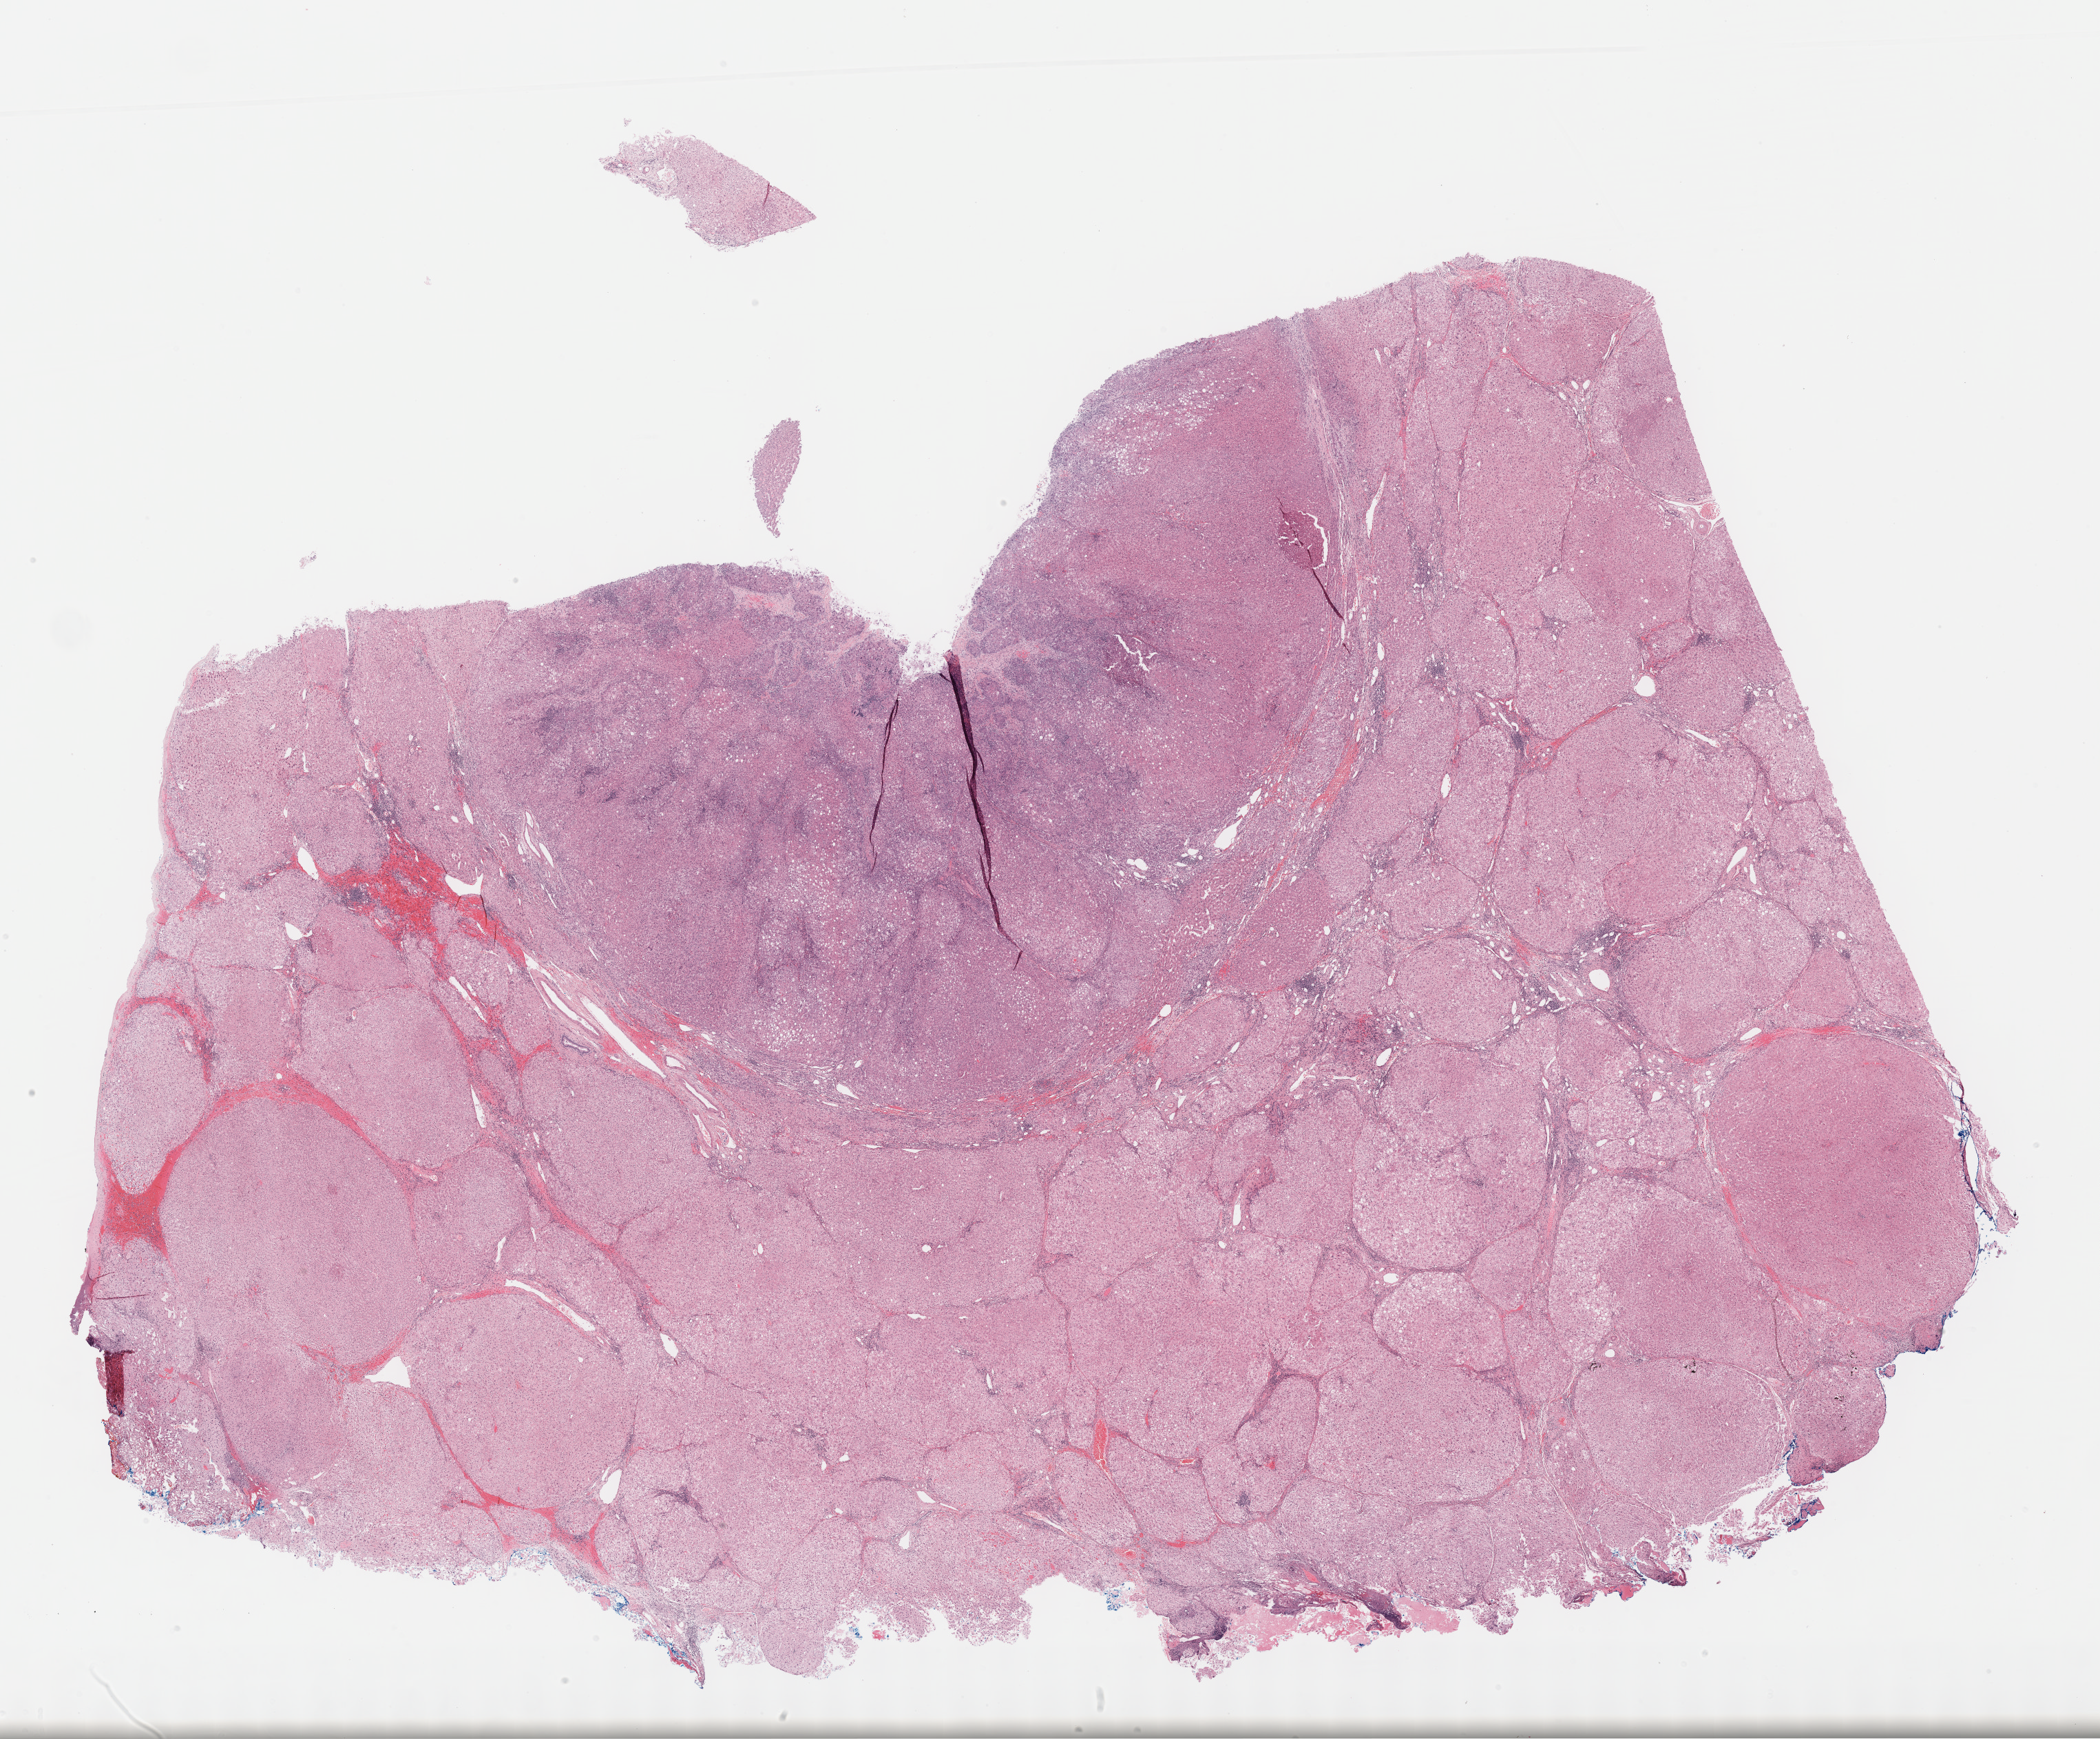
Whole-slide histology image, H&E, whole scanned area (about 24.7 x 20.4 mm, acquisition: 40x scan) shown as a low-resolution overview. Formalin-fixed paraffin-embedded (FFPE) diagnostic section. Primary tumour sample from the liver. Male patient; age at initial diagnosis 68 years. Histologic grade: G2 (moderately differentiated).
- histologic diagnosis: Hepatocellular carcinoma, NOS
- AJCC pathologic stage: I (7th edition)